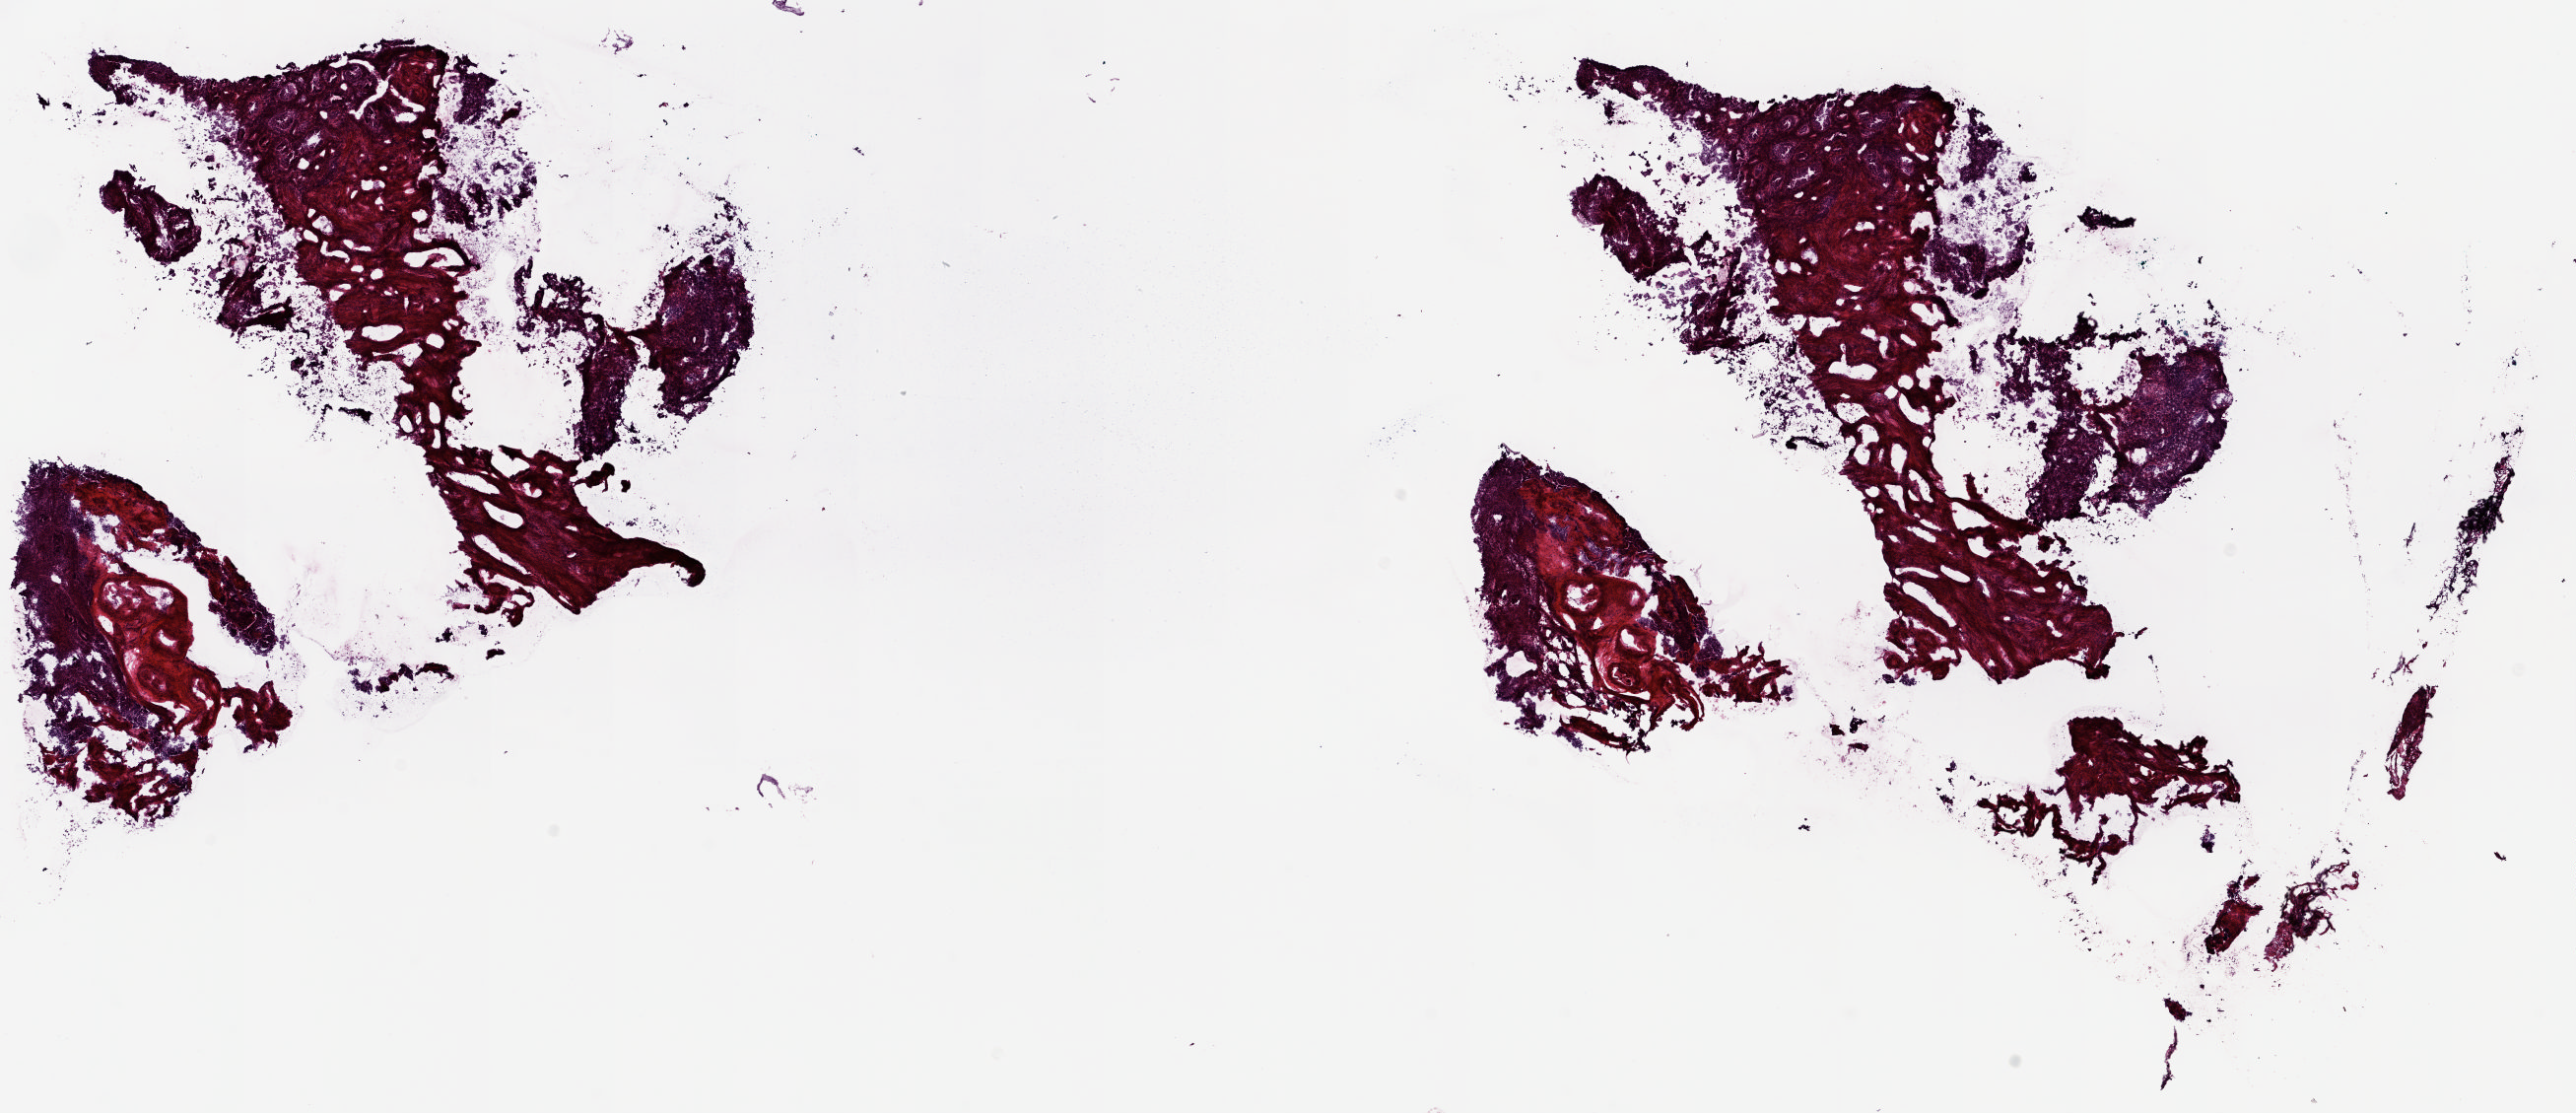
Whole-slide histology image, H&E-stained — whole scanned area (about 20.8 x 9.0 mm) shown as a low-resolution overview. Frozen section from the top of the tissue portion. Uterus, solid tissue normal (non-tumour tissue) sample. Composition of this section per pathologist review: tumour cells 0%, normal cells 100%.
This section: solid tissue normal (non-tumour) sample.